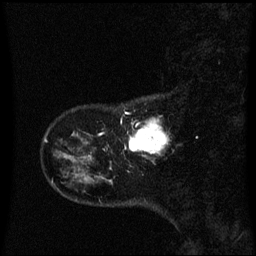
Breast MRI (dynamic contrast-enhanced), one sagittal slice. Dynamic contrast-enhanced series, image 2 of 3 at this slice position (ordered by acquisition). 1.5 T. TE 4.2 ms, TR 8.4 ms. 2 mm slice thickness. 256 × 256 image matrix, field of view 220 × 220 mm. Female patient, age 41 years. From the clinical record (not read from this slice): setting: breast cancer imaged before/during neoadjuvant chemotherapy; receptor status: triple-negative.
Outlined on this slice (semi-automatic segmentation, software-assisted and operator-edited):
- analysis volume of interest (the breast-tissue region the enhancement analysis was run in; not a lesion): bounding box <124,110,166,167> (left, top, right, bottom; pixels)
- tumour enhancement mask (voxels above the 70 % enhancement threshold inside the analysis volume of interest): <130,124,166,153>